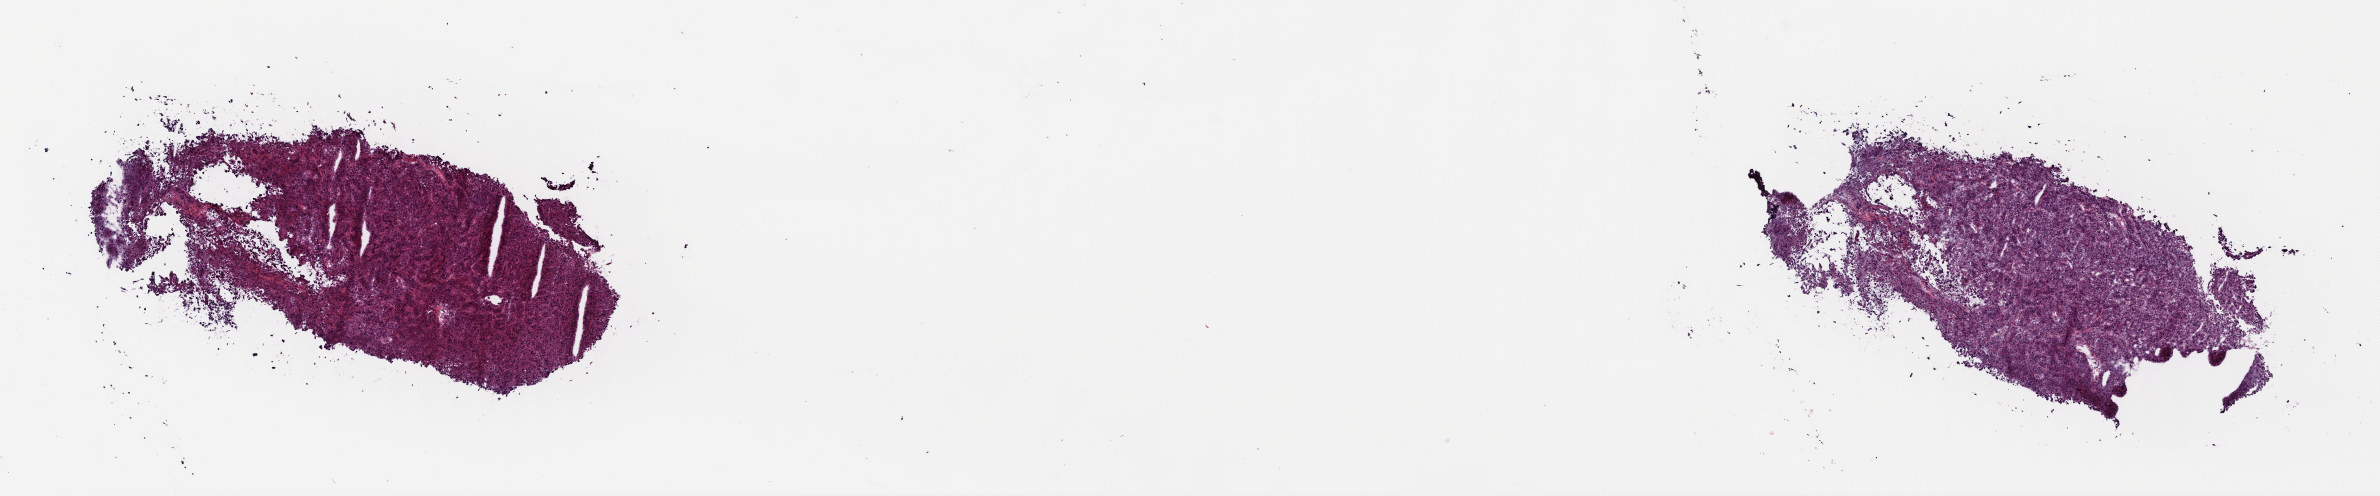
Digitized H&E tissue section (whole slide) — low-resolution overview of the scanned area, about 18.7 x 3.9 mm (acquisition: 40x scan). Frozen section from the top of the tissue portion. Primary tumour sample from the adrenal cortex. Female, age 31 years at initial diagnosis. Composition of this section per pathologist review: tumour cells 100%, tumour nuclei 80%, normal cells 0%, stromal cells 0%, necrosis 0%. Inflammatory infiltration, as recorded: lymphocyte infiltration 1%, monocyte infiltration 0%, neutrophil infiltration 0%.
* diagnosis: Adrenal cortical carcinoma (cortex of adrenal gland)